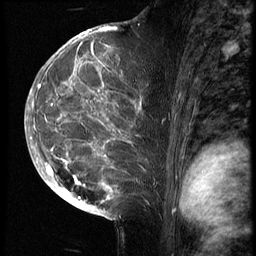
Breast MRI (dynamic contrast-enhanced), one sagittal slice. Slice 38 of 70 in the series (ordered by position). 3 images stored at this slice position (order not interpretable as contrast timing). 1.5 T. TE 4.2 ms, TR 9 ms. 2.5 mm slice thickness. 256 × 256 image matrix, field of view 180 × 180 mm. Patient: female, 28 years. Case-level facts recorded for this patient, not image findings: setting: breast cancer imaged before/during neoadjuvant chemotherapy.
Annotated regions visible in this slice (semi-automatic segmentation, software-assisted and operator-edited):
- analysis volume of interest (the breast-tissue region the enhancement analysis was run in; not a lesion): bounding box (x1, y1, x2, y2) in pixels: (43, 42, 162, 215)
- tumour enhancement mask (voxels above the 140 % enhancement threshold inside the analysis volume of interest): (46, 42, 129, 204)